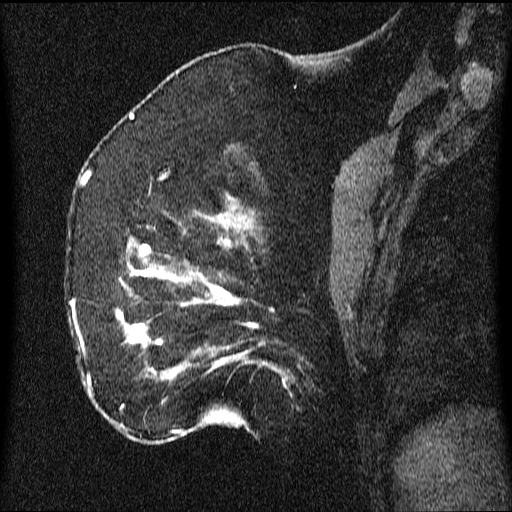
Breast MRI (dynamic contrast-enhanced), one sagittal slice; position 19 of 64 along the scan axis; dynamic contrast-enhanced series, image 2 of 3 at this slice position (ordered by acquisition); 1.5 T; TE 4.2 ms, TR 9.1 ms; 2.2 mm slice thickness; 512 × 512 image matrix, field of view 180 × 180 mm. Patient: female, 52 years.
Outlined on this slice (semi-automatically segmented with operator editing):
- analysis volume of interest (the breast-tissue region the enhancement analysis was run in; not a lesion): bounding box <65,203,350,438> (left, top, right, bottom; pixels)
- tumour enhancement mask (voxels above the 70 % enhancement threshold inside the analysis volume of interest): <72,207,287,436>